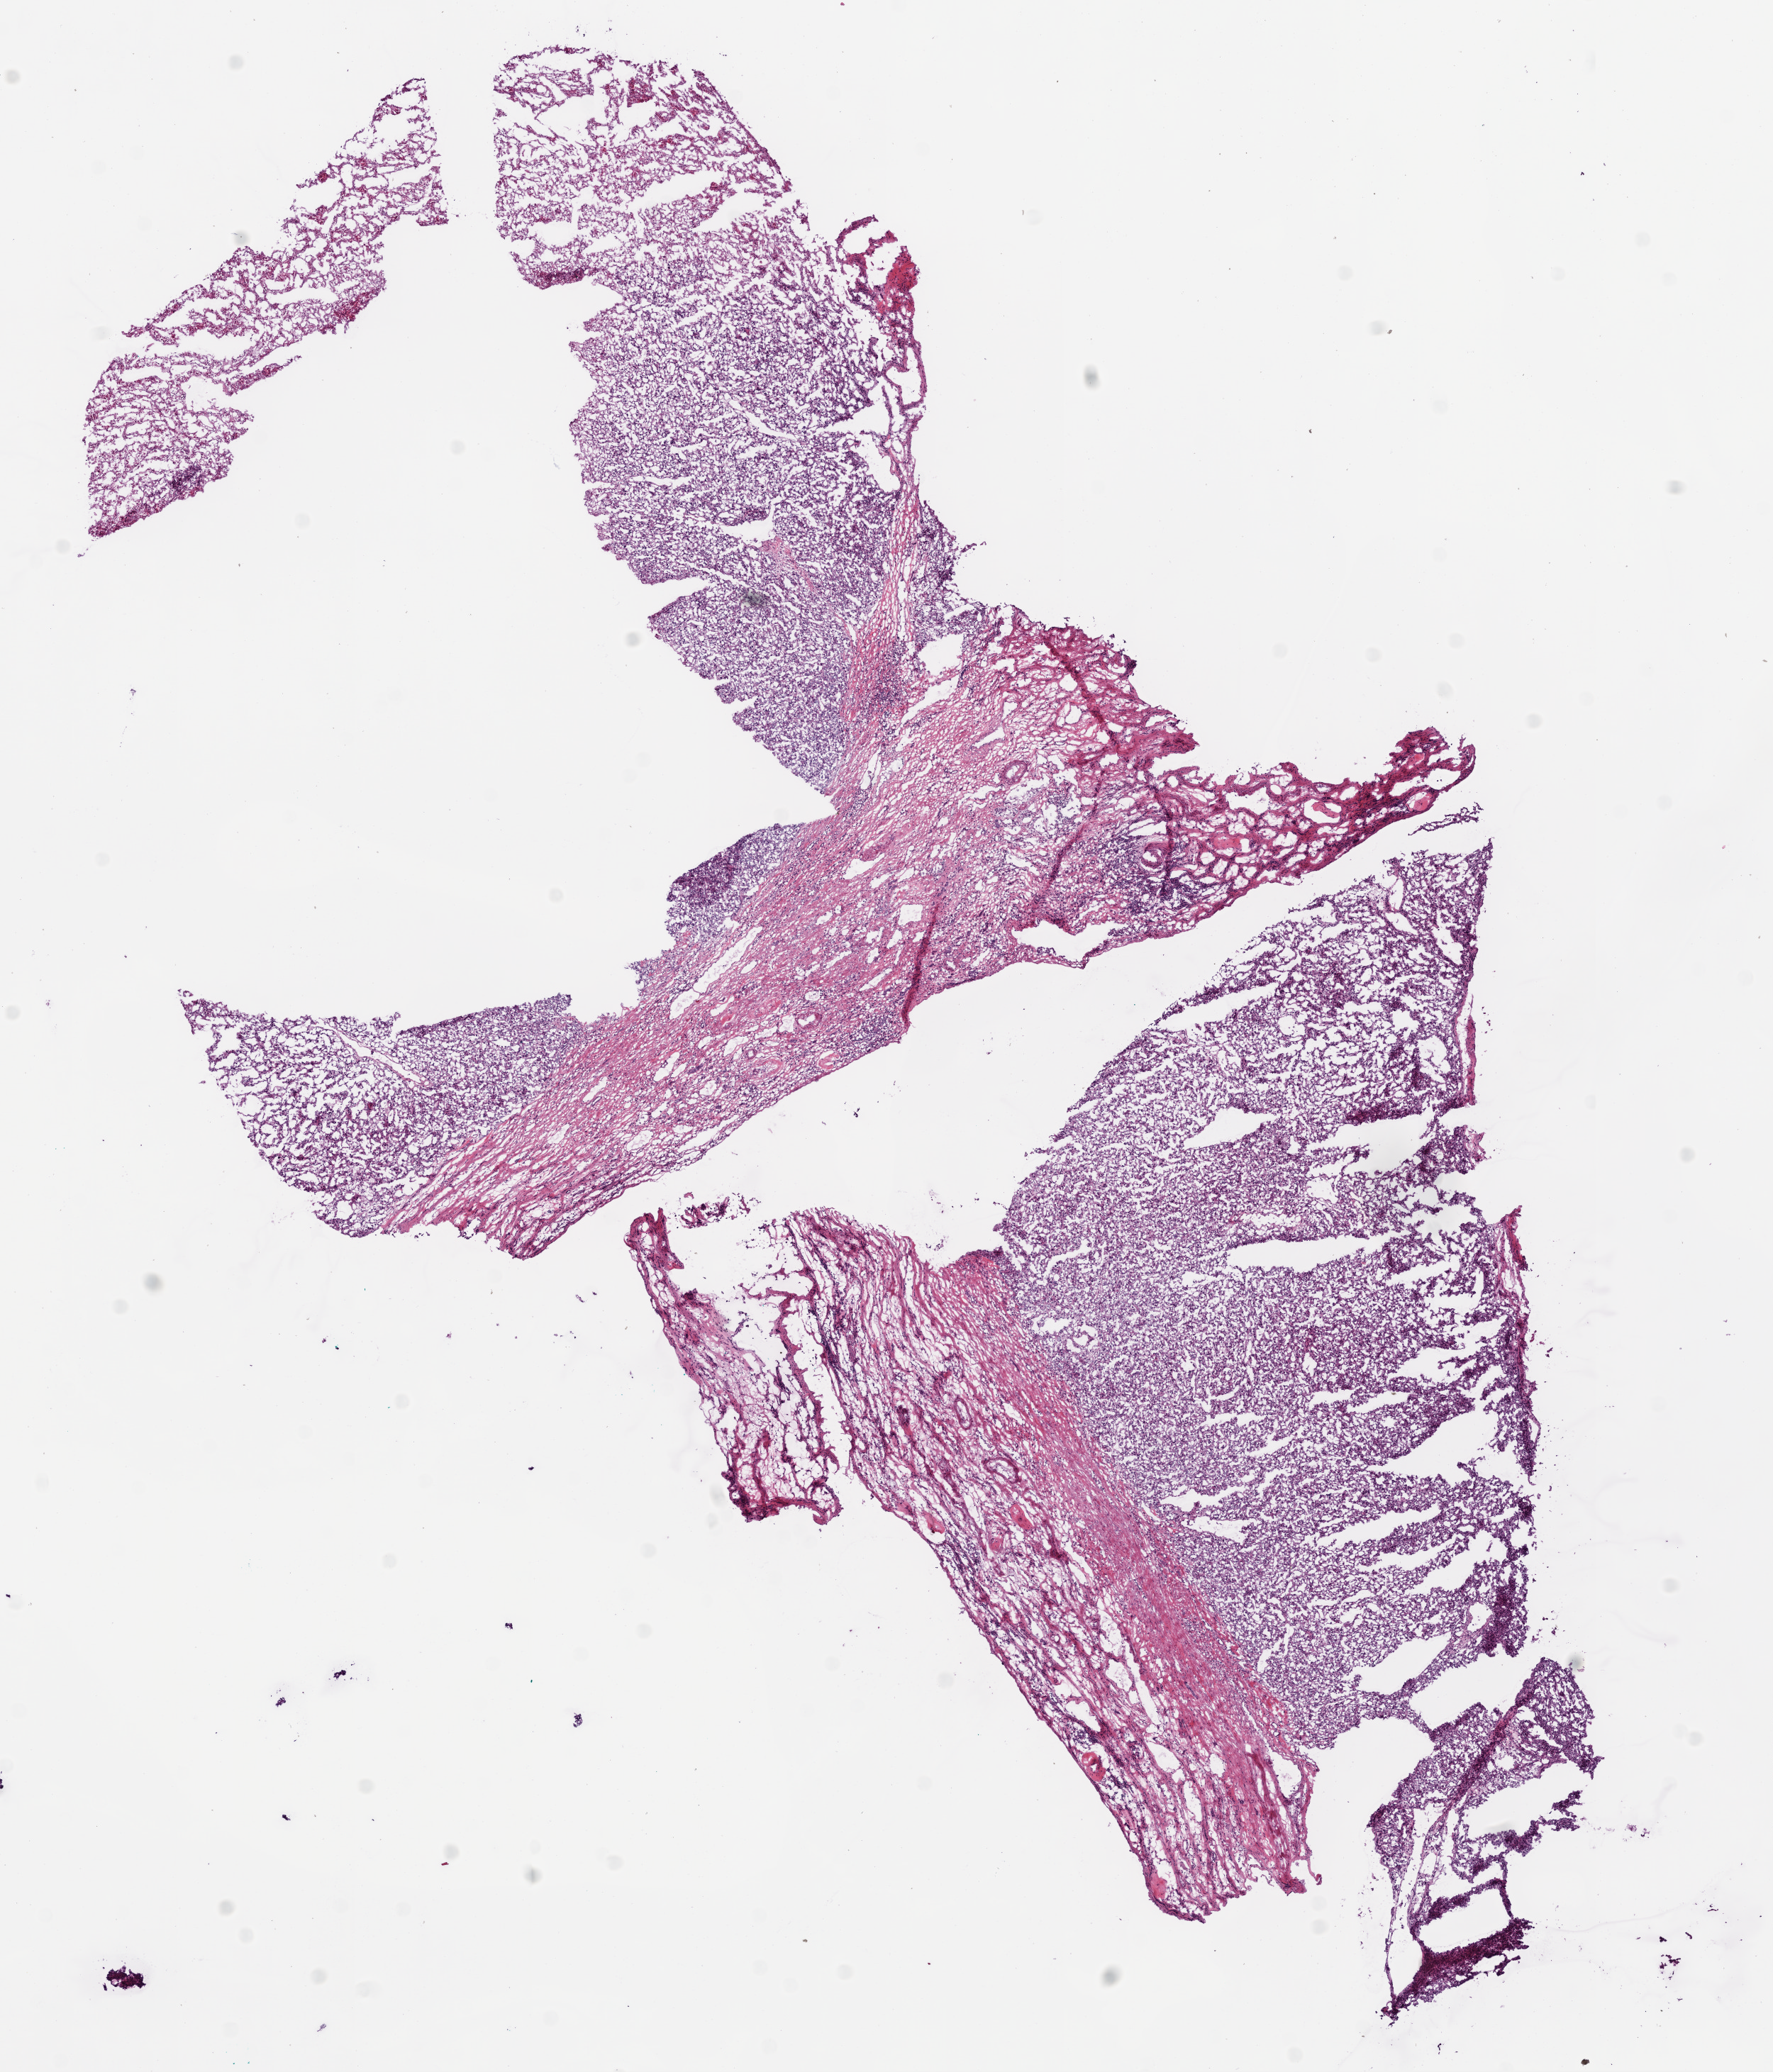
Digitized H&E-stained tissue section (whole slide), a low-resolution overview of the entire scanned area, about 10.0 x 11.7 mm (from a 20x scan), frozen section, primary tumour sample from the kidney. Patient: male, age at initial diagnosis 48 years. Histologic grade: G3 (poorly differentiated). Slide review estimates, as recorded: tumour cells 80%, tumour nuclei 65%, normal cells 20%, stromal cells 0%, necrosis 0%.
* laterality: right
* AJCC pathologic stage: I
* diagnosis: Clear cell adenocarcinoma, NOS